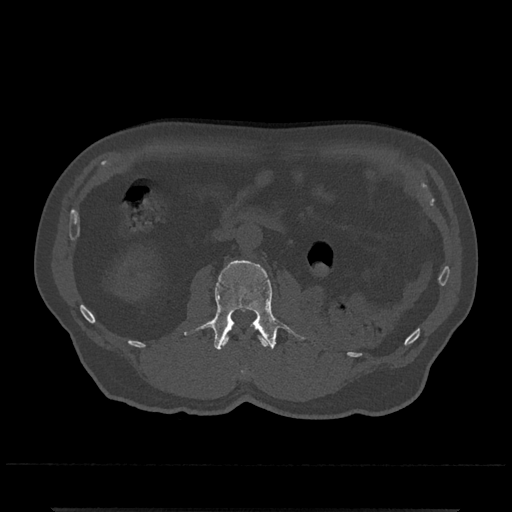
CT including the spine, one axial slice. Position 303 of 797 along the scan axis. Bone window (W 1800 / L 400 HU). 0.5 mm slice thickness. 512 × 512 image matrix, field of view 393 × 393 mm. Male patient, age 67 years. Case-level facts recorded for this patient, not image findings: primary cancer: prostate.
Structures marked on this image (semi-automatically segmented with operator editing):
- L1 vertebra: bounding box [x1, y1, x2, y2] px = [222, 336, 269, 374]
- L2 vertebra: [184, 260, 306, 350]